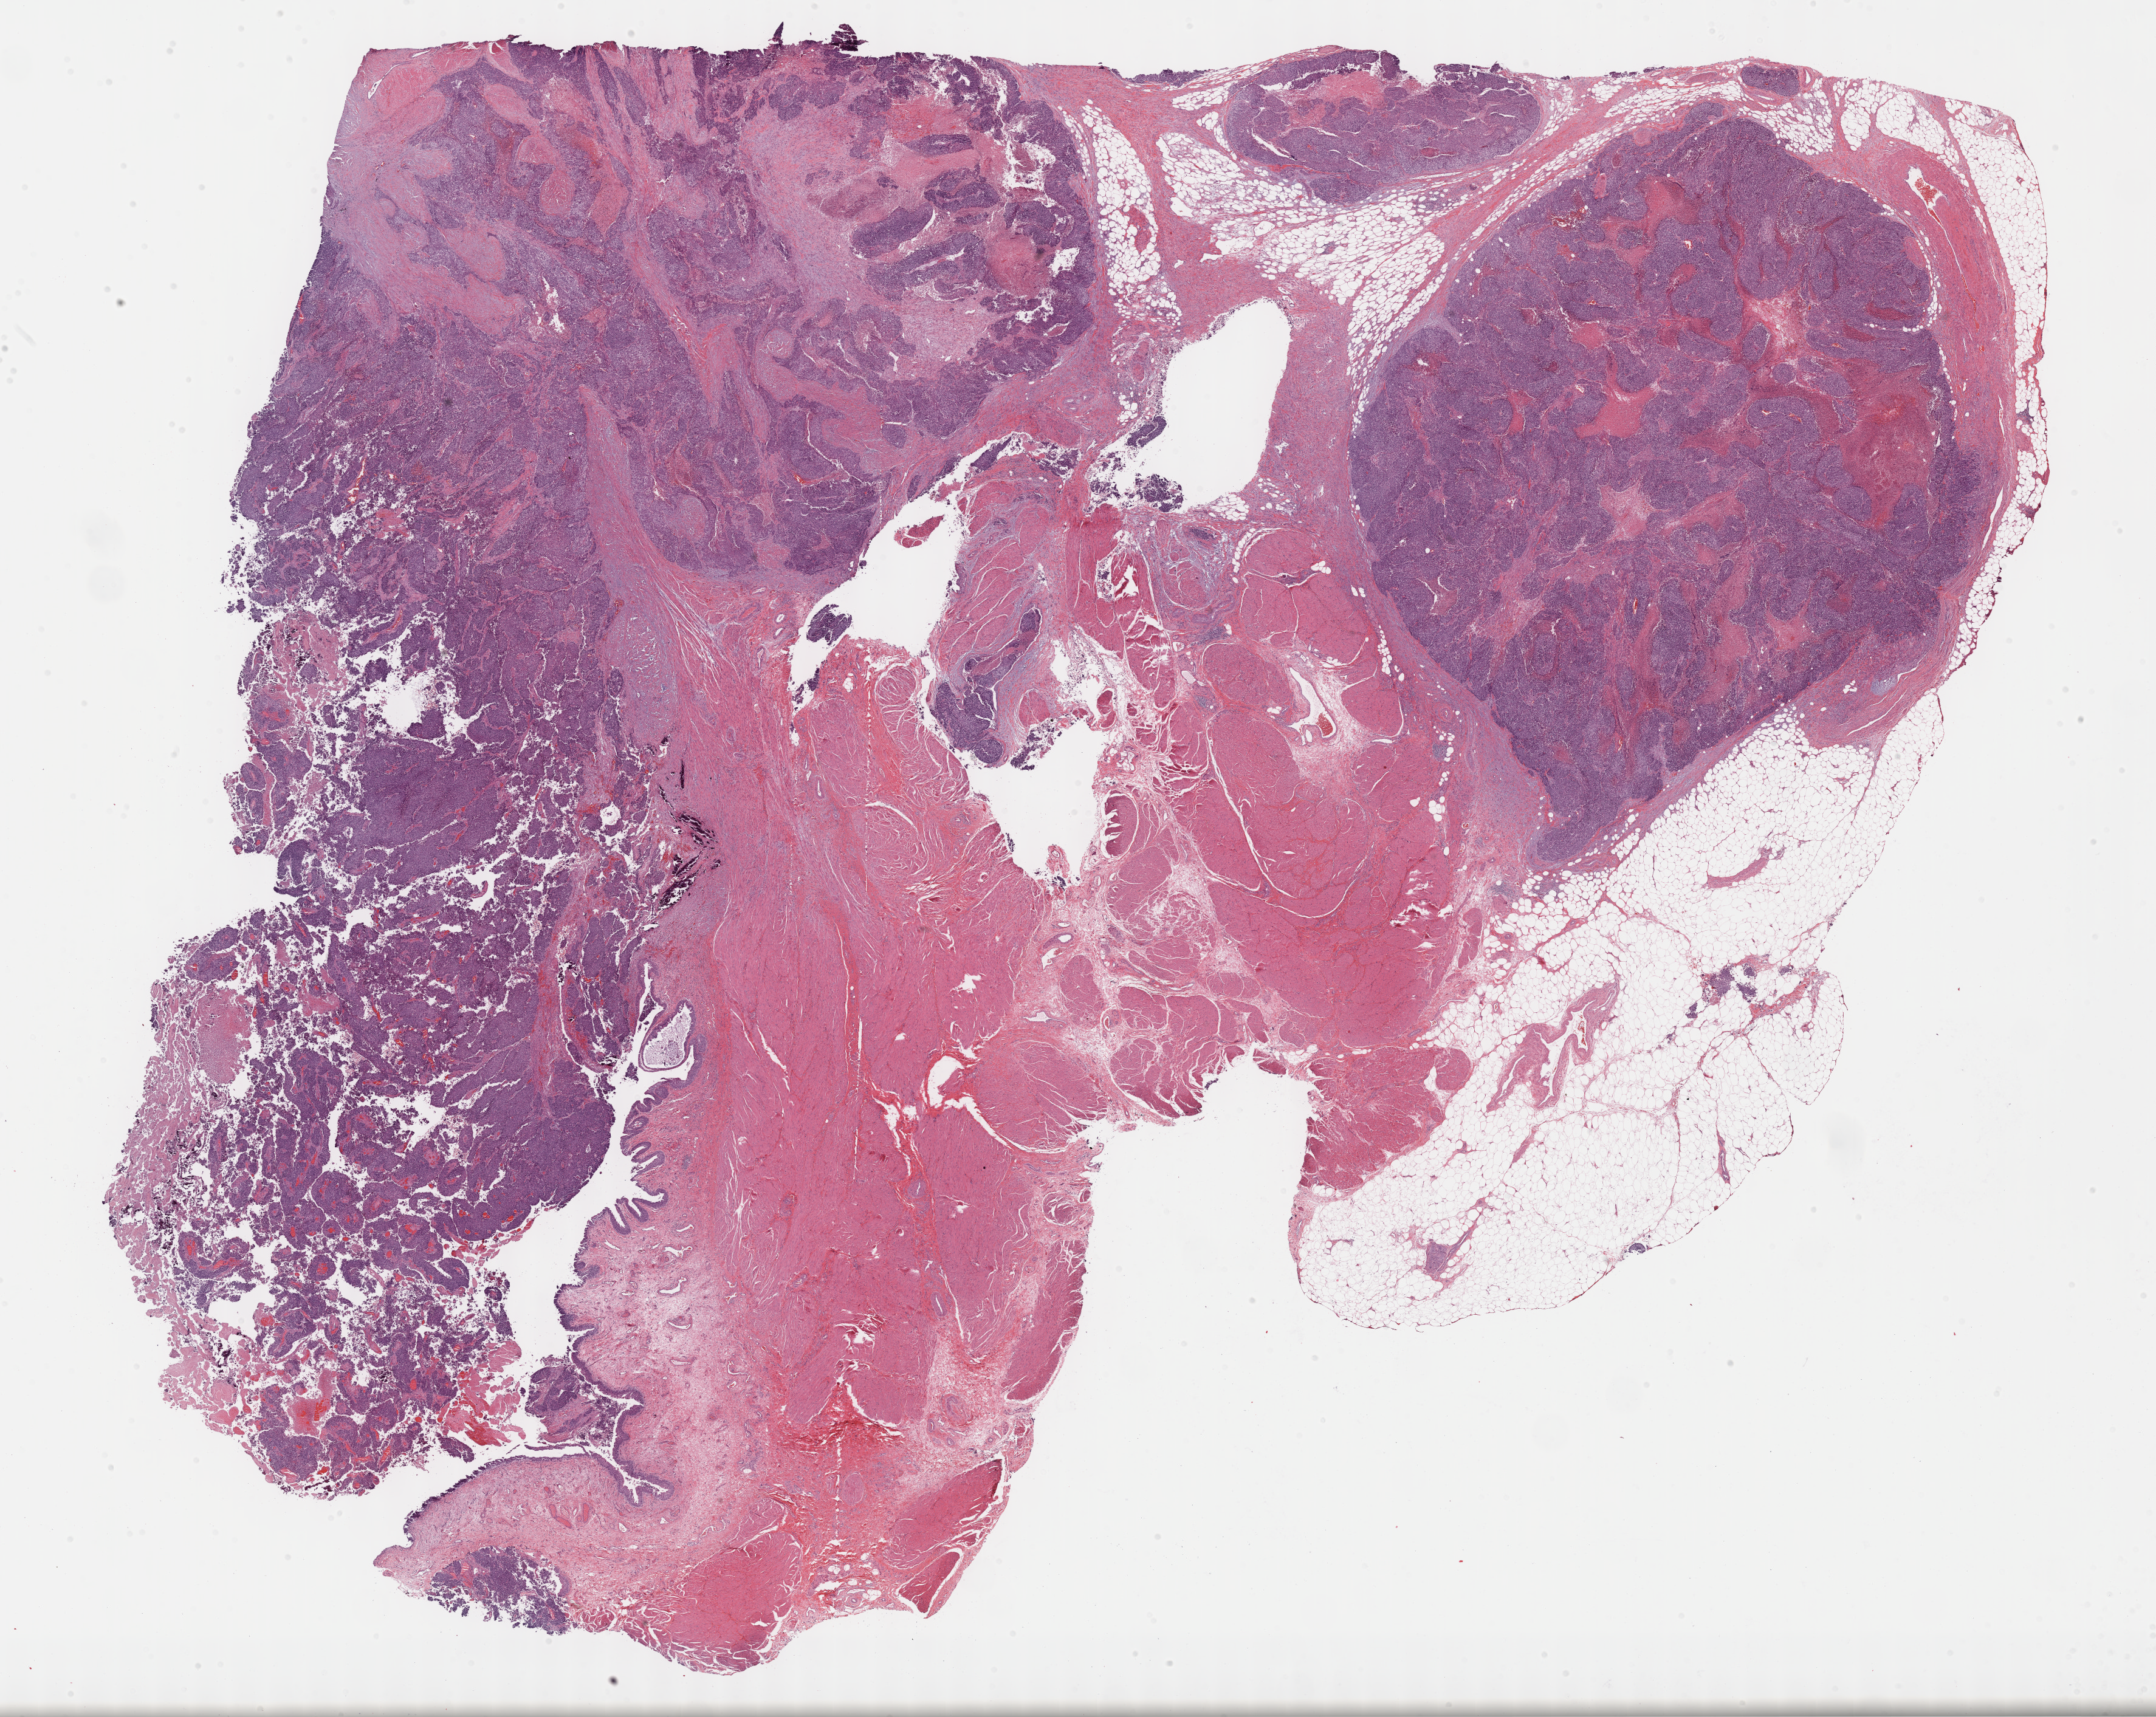
Digitized H&E tissue section (whole slide), shown as a low-resolution overview of the whole scanned area (about 28.7 x 22.9 mm); FFPE section; primary tumour sample from the bladder. Male, age 54 years at initial diagnosis.
Histologic diagnosis: Transitional cell carcinoma.